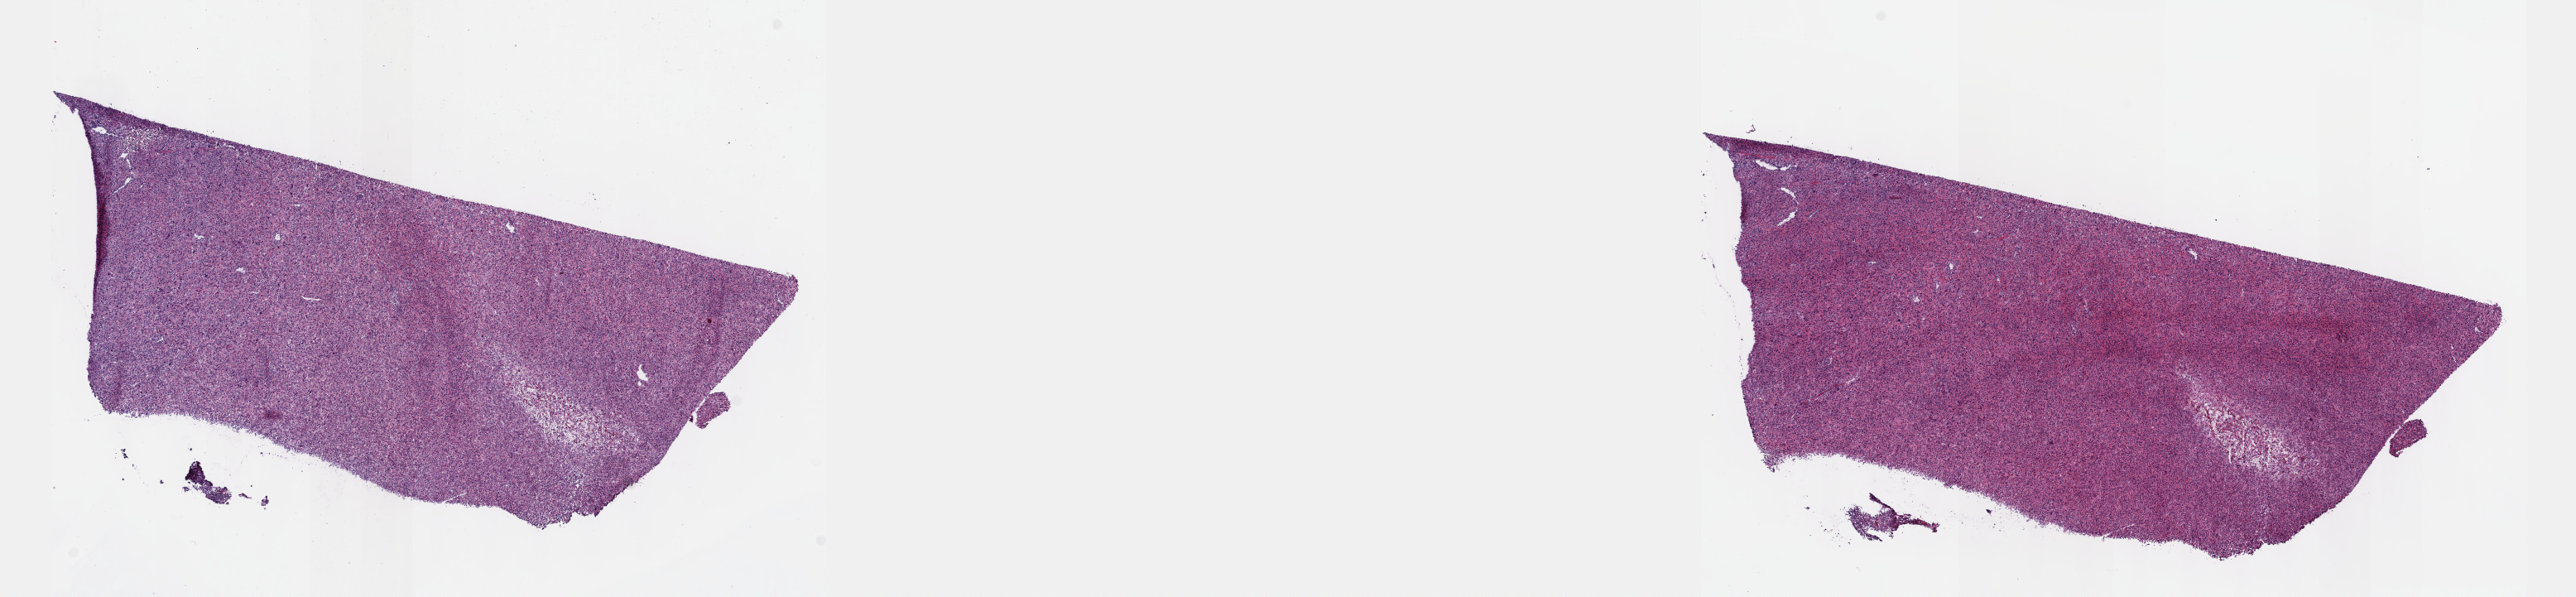
Digitized H&E-stained tissue section (whole slide) — low-resolution overview of the scanned area, about 25.1 x 5.8 mm; frozen section from the top of the tissue portion; sample: primary tumour, connective, subcutaneous and other soft tissues. Patient sex: female. Composition of this section per pathologist review: tumour cells 100%, tumour nuclei 80%, normal cells 0%, stromal cells 0%, necrosis 0%. Inflammatory infiltration, as recorded: lymphocyte infiltration 1%, monocyte infiltration 0%, neutrophil infiltration 0%.
Pathologic diagnosis: Malignant fibrous histiocytoma (connective, subcutaneous and other soft tissues of trunk, NOS).